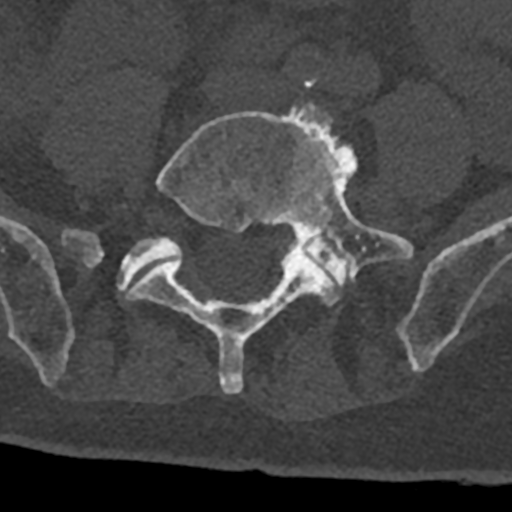
CT including the spine, one axial slice; slice 196 of 797 in the series (ordered by position); reconstruction kernel Br40s/3; 120 kVp; bone window (W 1800 / L 400 HU); 512 × 512 image matrix, field of view 160 × 160 mm. Male patient, age 74 years. Case-level facts recorded for this patient, not image findings: primary cancer: renal; vertebrae with lytic lesions (as recorded): T10, L1, L2, L3, L4, L5.
Annotated regions visible in this slice (semi-automatic segmentation, software-assisted and operator-edited):
- L5 vertebra: bounding box (x1, y1, x2, y2) in pixels: (126, 102, 413, 394)